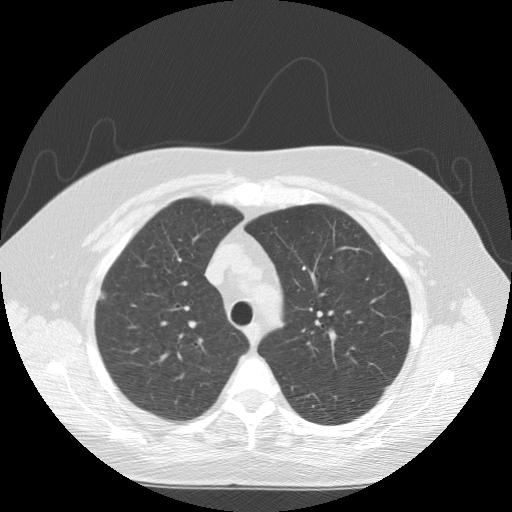
Low-dose screening chest CT, axial slice. First (baseline) screen. Lung window (W 1500 / L -600 HU). Slice 35 of 146 in the series. 512 × 512 image matrix. Female, age 55 years at enrolment. Current smoker at enrolment.
- Lesion marked by an expert reader, bounding box <87,280,121,318> (left, top, right, bottom; pixels).
- Screening reader's record for this exam (one nodule recorded; not confirmed to be the boxed lesion): non-calcified nodule or mass ≥4 mm, right upper lobe, 8 × 7 mm, spiculated (stellate) margins, soft tissue attenuation.
- Official screen result: positive, change unspecified: nodule(s) >= 4 mm or enlarging nodule(s), mass(es), or other non-specific abnormalities suspicious for lung cancer.